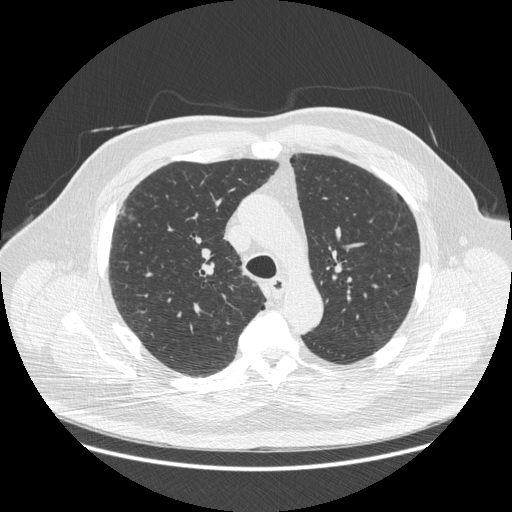
Axial slice from a low-dose chest CT screening exam. First (baseline) screen. Lung window (W 1500 / L -600 HU). Standard (soft-tissue) reconstruction kernel (STANDARD). 512 × 512 image matrix. Male participant, aged 66 years at enrolment. Current smoker at enrolment.
Expert-annotated lung lesion, bounding box [x1, y1, x2, y2] px = [110, 204, 145, 232]. Screening reader's record for this exam: no non-calcified nodule ≥4 mm recorded. Official screen result: negative screen, no significant abnormalities. Lung cancer was diagnosed 742 days after this screen: non-small cell carcinoma, right upper lobe, stage IV (AJCC 6th edition), 50 mm at pathology.